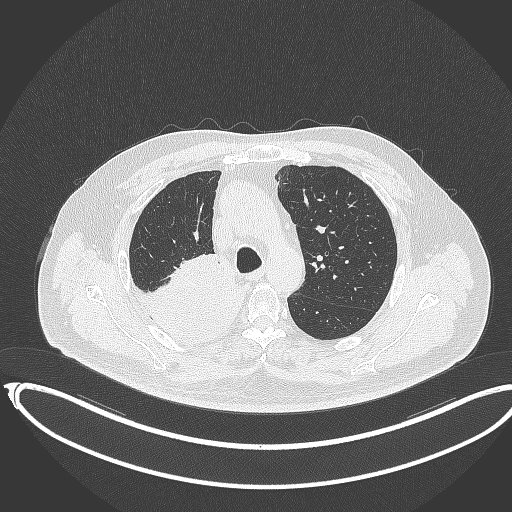
Chest CT, one axial slice. Slice 258 of 403 in the series (ordered by position). Reconstruction kernel B70f. 120 kVp. Lung window (W 1500 / L -600 HU). 1 mm slice thickness. 512 × 512 image matrix, field of view 436 × 436 mm. Male patient, age 68 years. From the clinical record (not read from this slice): clinical TNM (as recorded): T2a N0 M0.
Annotated regions visible in this slice (bounding box drawn by a radiologist):
- lung tumour (recorded histology: adenocarcinoma): bounding box [x1, y1, x2, y2] px = [128, 256, 246, 340]